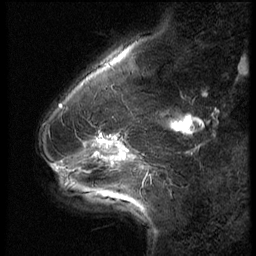
Breast MRI (dynamic contrast-enhanced), one sagittal slice; position 16 of 62 along the scan axis; 3 images stored at this slice position (order not interpretable as contrast timing); 1.5 T; TE 4.2 ms, TR 9 ms; 2.5 mm slice thickness; 256 × 256 image matrix. Patient: female, 54 years. Case-level facts recorded for this patient, not image findings: setting: breast cancer imaged before/during neoadjuvant chemotherapy; receptor status: HR-positive, HER2-negative.
Outlined on this slice (semi-automatically segmented with operator editing):
- analysis volume of interest (the breast-tissue region the enhancement analysis was run in; not a lesion): bounding box [x1, y1, x2, y2] px = [42, 126, 146, 183]
- tumour enhancement mask (voxels above the 140 % enhancement threshold inside the analysis volume of interest): [94, 139, 111, 156]